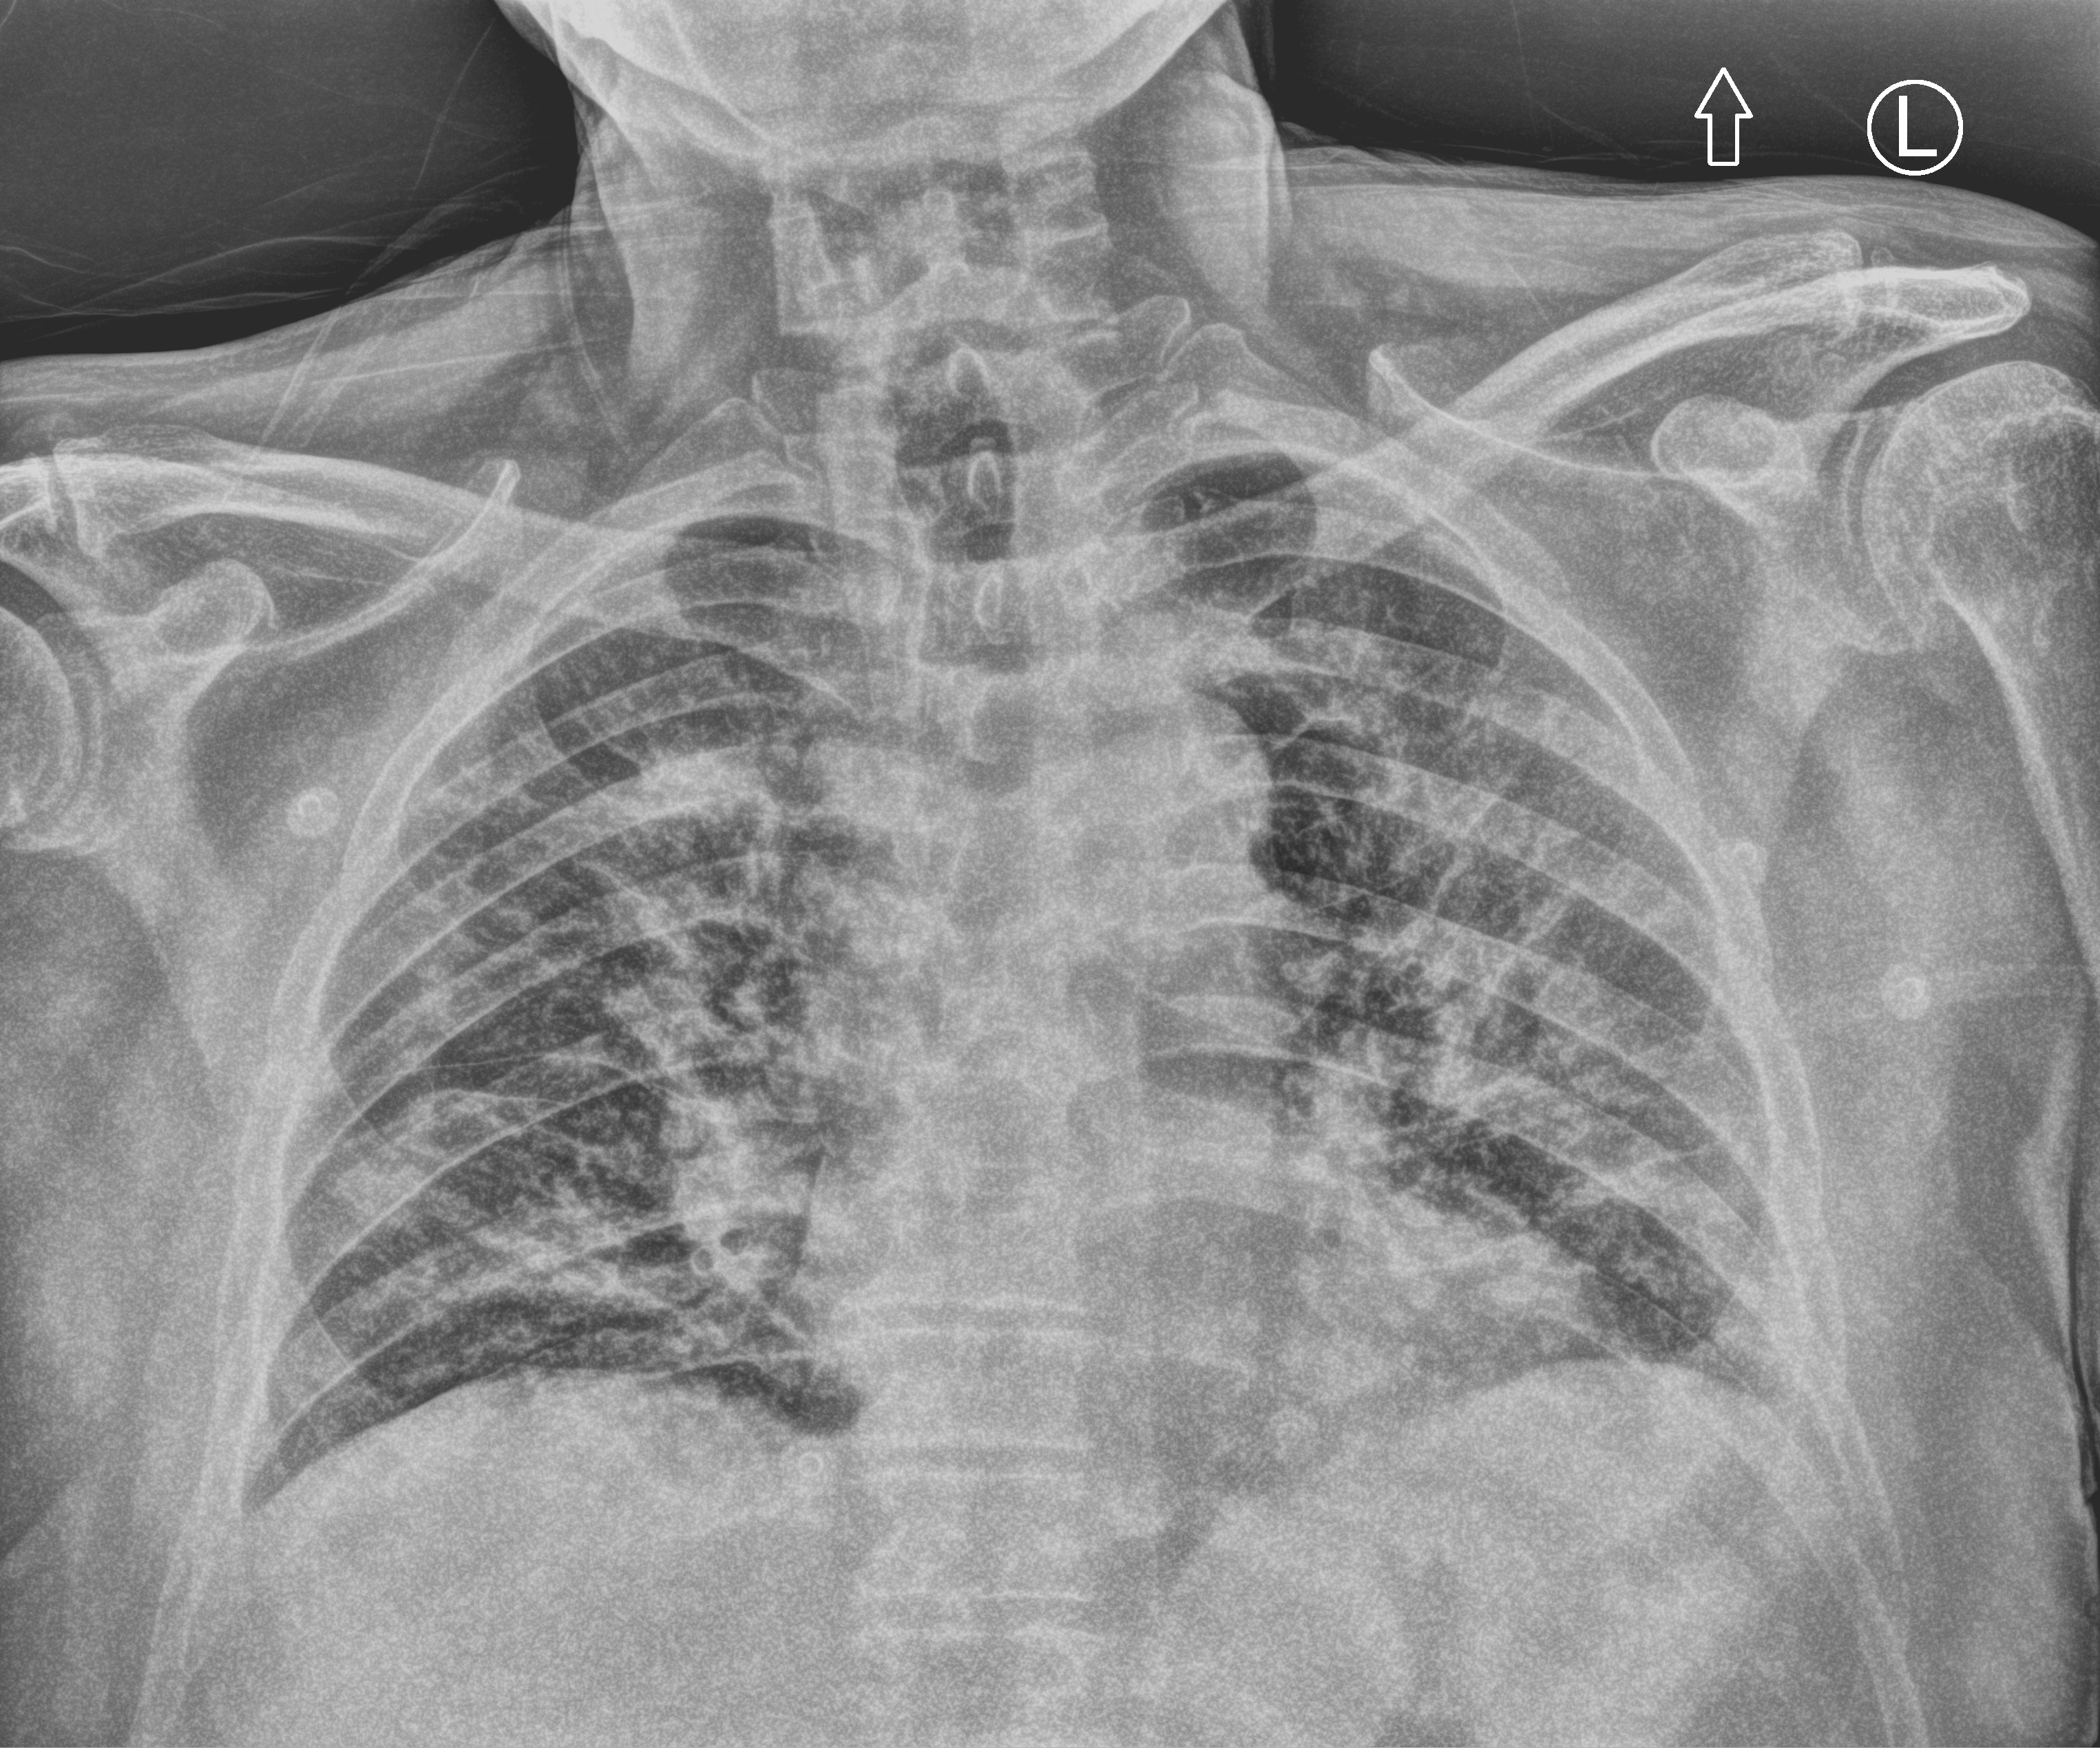
Chest X-ray (portable), anteroposterior (AP) projection. Patient hospitalised with COVID-19; male, aged 60–74 years.
Hospital-stay facts (about this admission, not read from this image; timing relative to this image not recorded):
- mechanically ventilated during this hospital stay: no